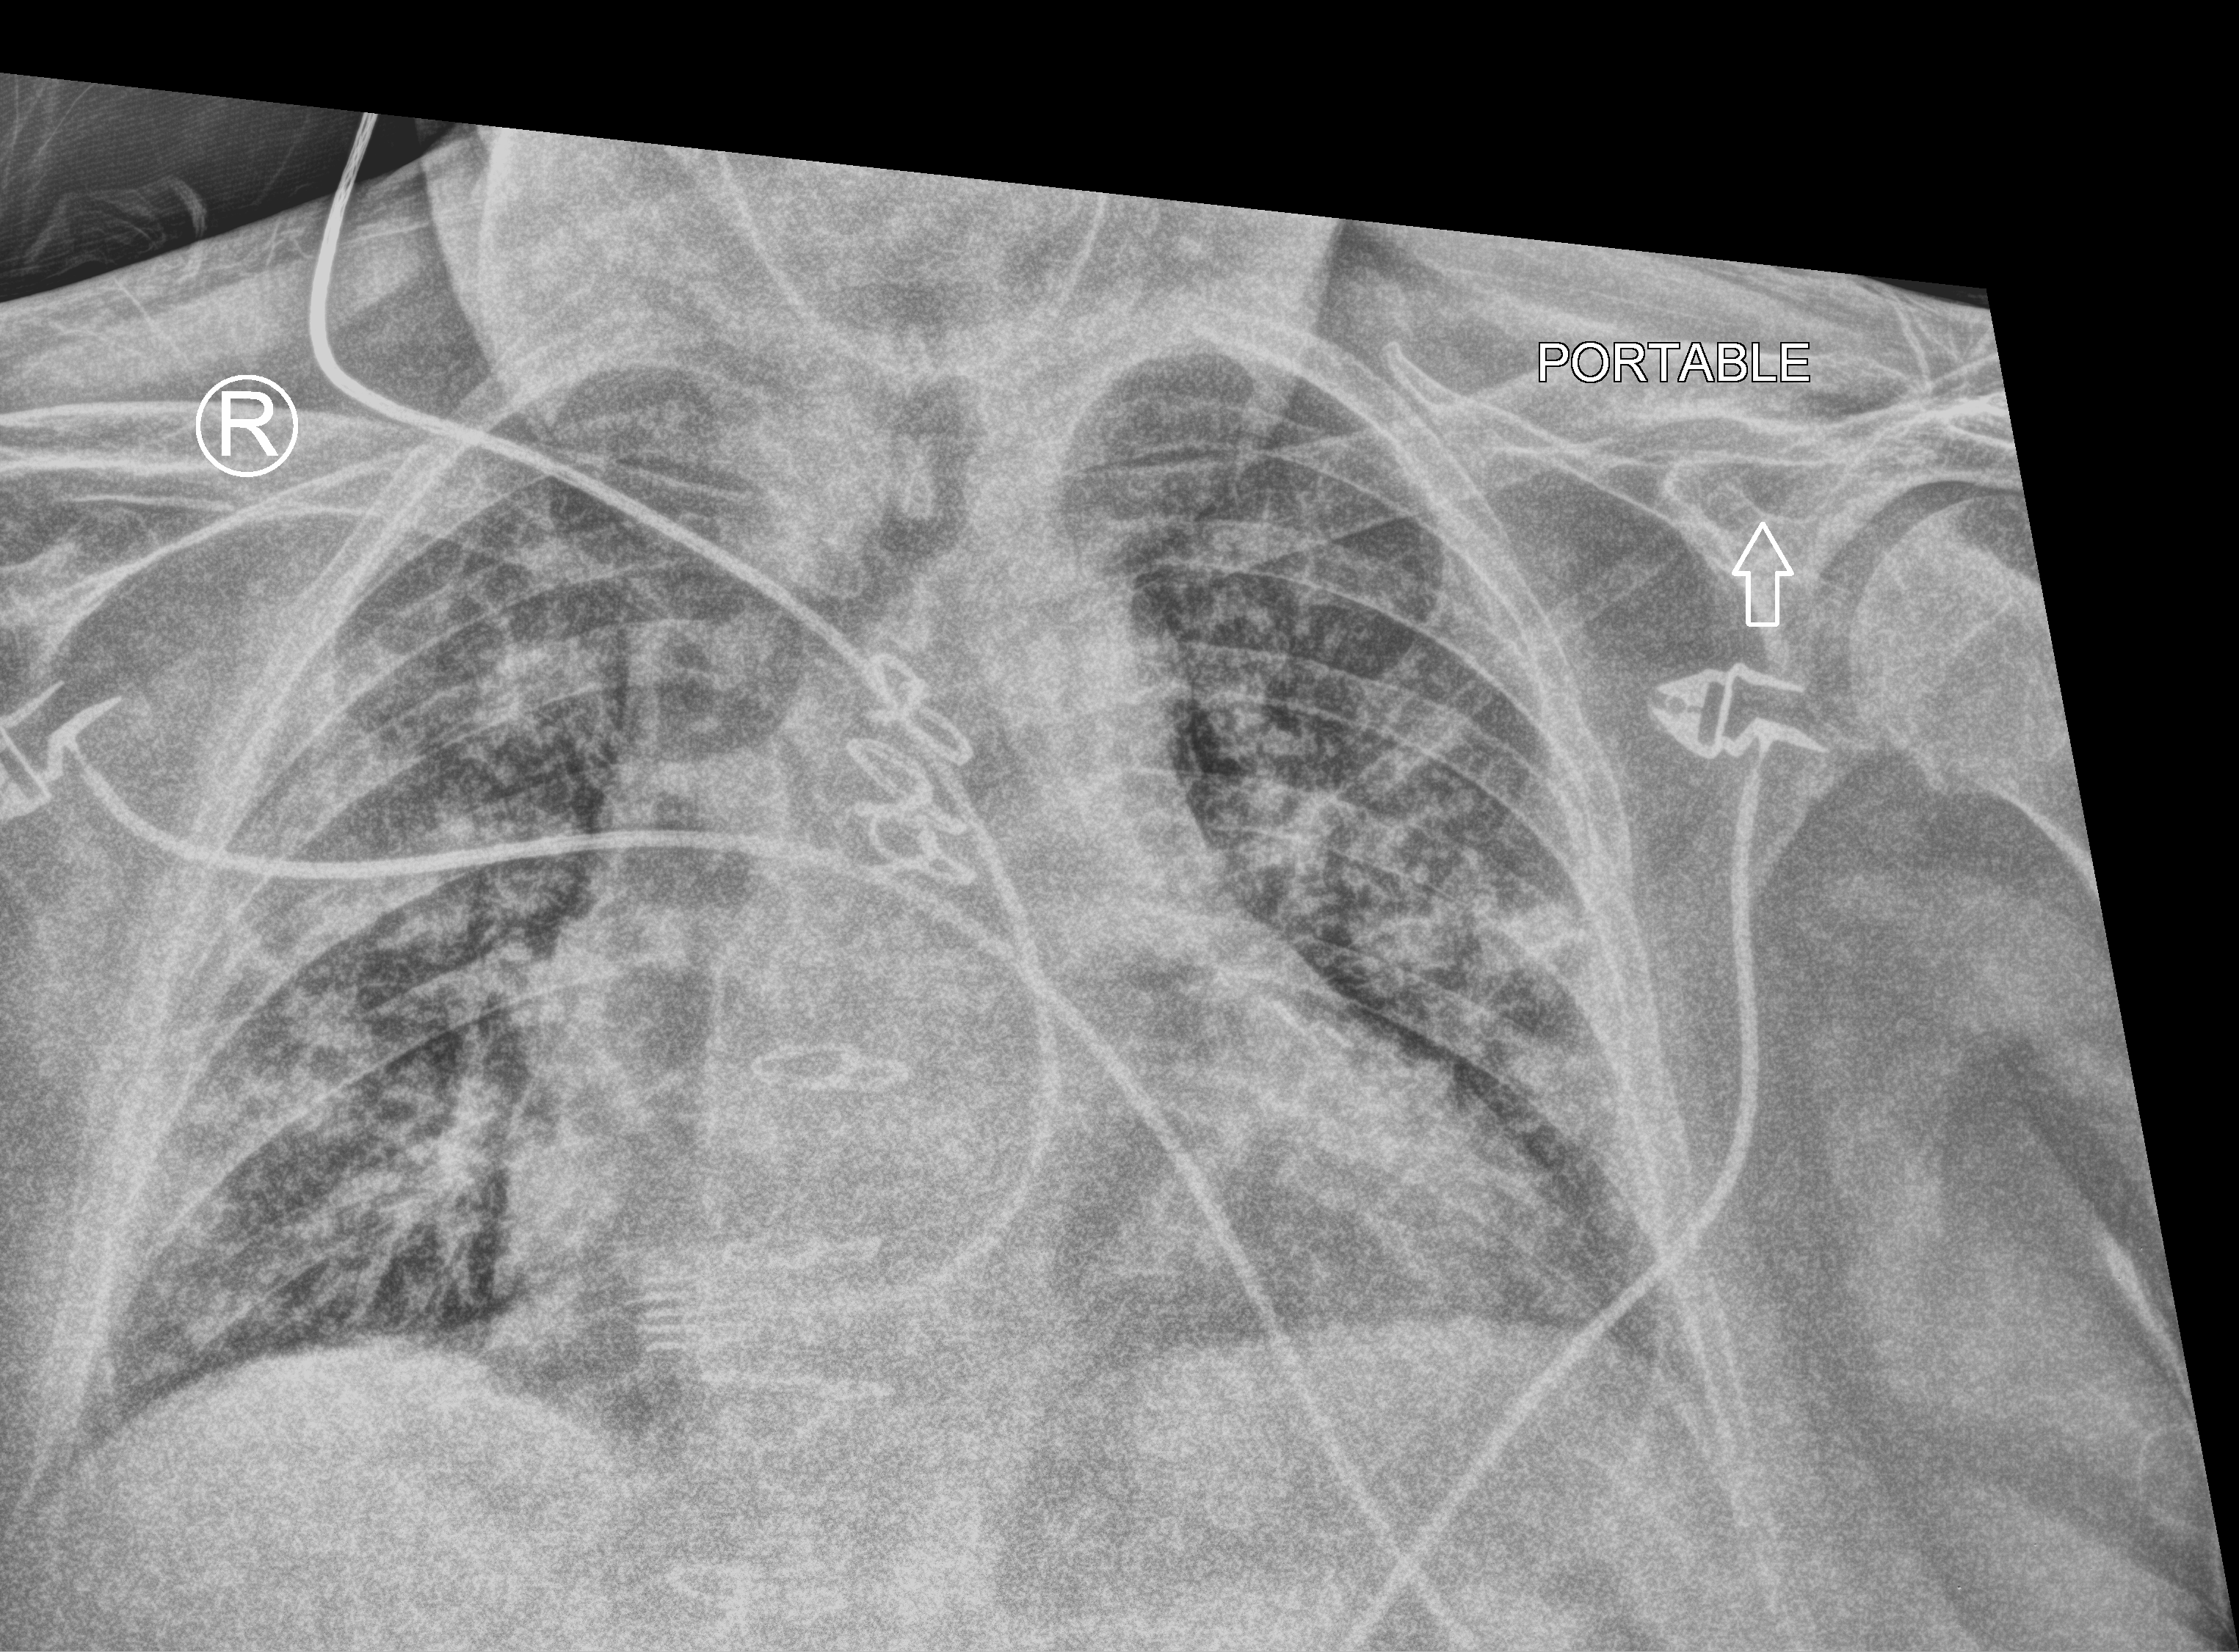
Chest X-ray (portable), anteroposterior (AP) projection. Male patient hospitalised with COVID-19, age 75–90 years.
Hospital-stay facts (about this admission, not read from this image; timing relative to this image not recorded):
- admitted to intensive care during this hospital stay: no